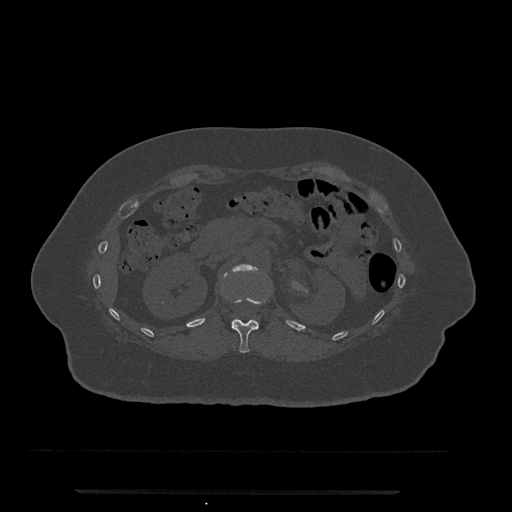
CT including the spine, one axial slice. Slice 146 of 797 in the series (ordered by position). Reconstruction kernel Br40s/3. Bone window (W 1800 / L 400 HU). 0.5 mm slice thickness. 512 × 512 image matrix. Patient: female, 51 years. Case-level facts recorded for this patient, not image findings: primary cancer: neuro.
Outlined on this slice (semi-automatic segmentation, software-assisted and operator-edited):
- L1 vertebra: bounding box (x1, y1, x2, y2) in pixels: (232, 264, 258, 272)
- T12 vertebra: (227, 297, 268, 353)